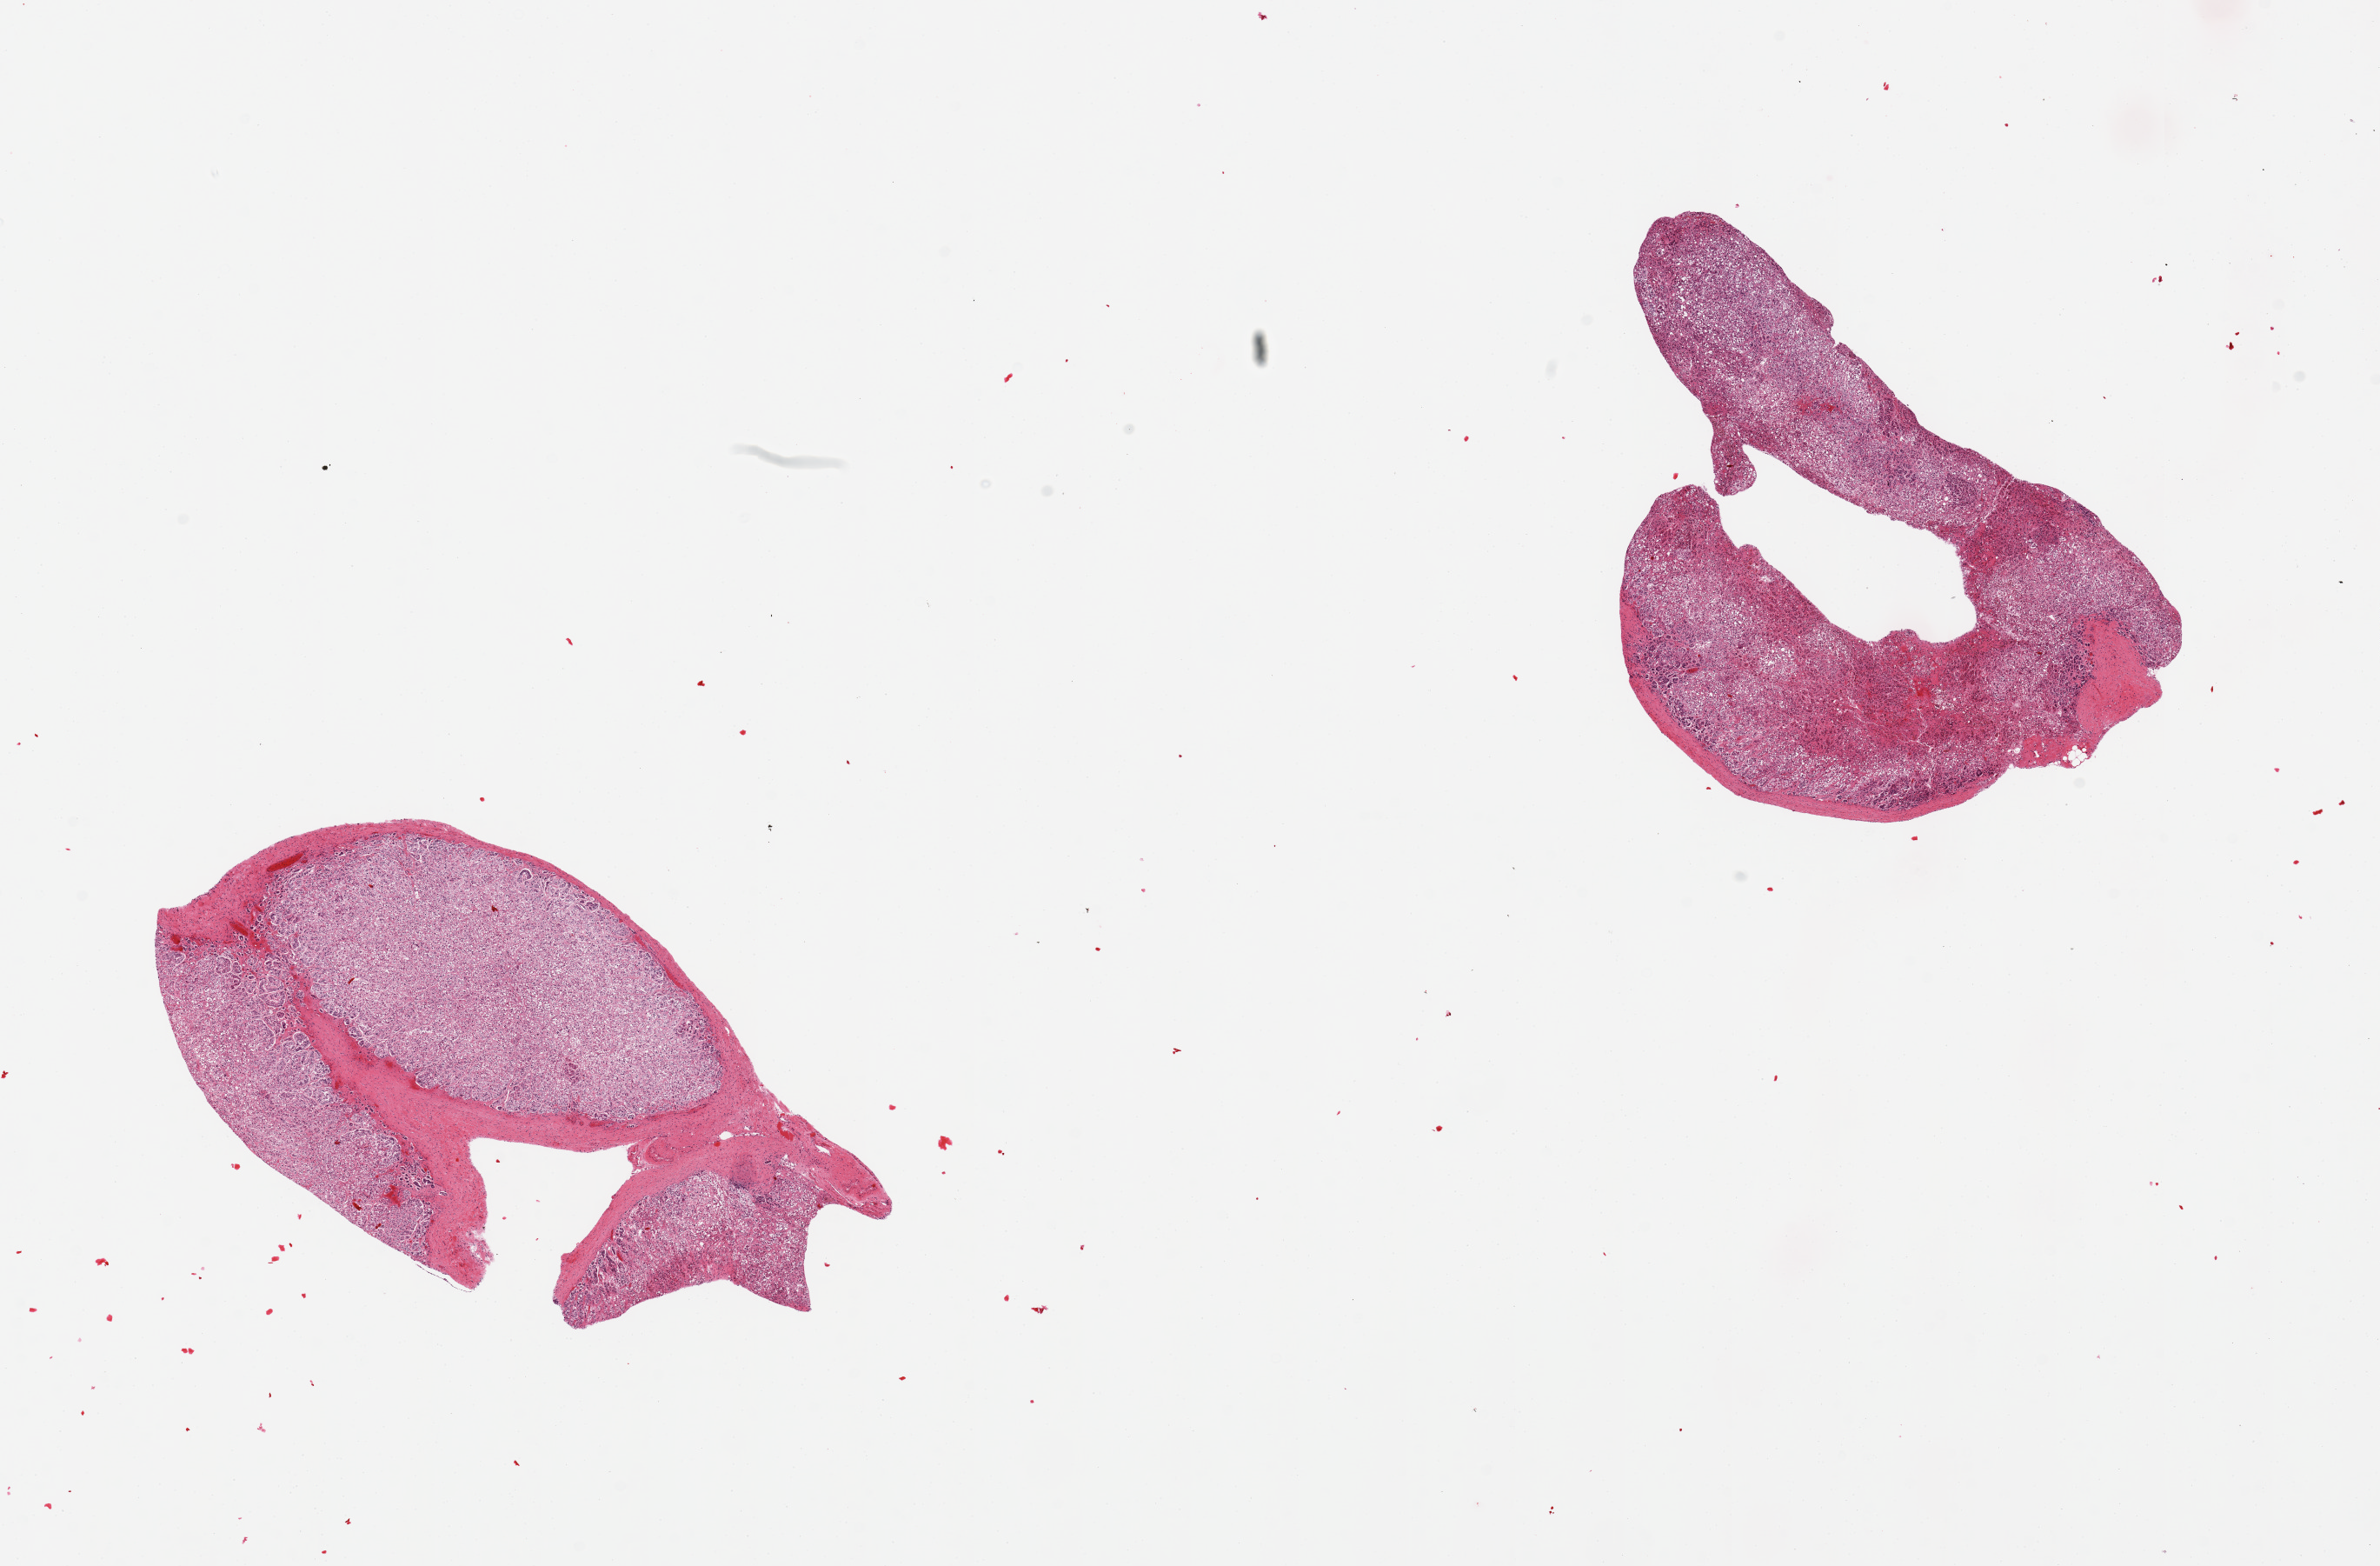
Digitized hematoxylin and eosin (H&E)-stained section, low-resolution overview of the scanned area, about 21.7 x 14.2 mm. PAXgene-fixed, paraffin-embedded tissue. Section of adrenal gland (target tissue). Tissue donor sample. Donor sex: male.
* reviewer comment on this tissue sample: 2 pieces